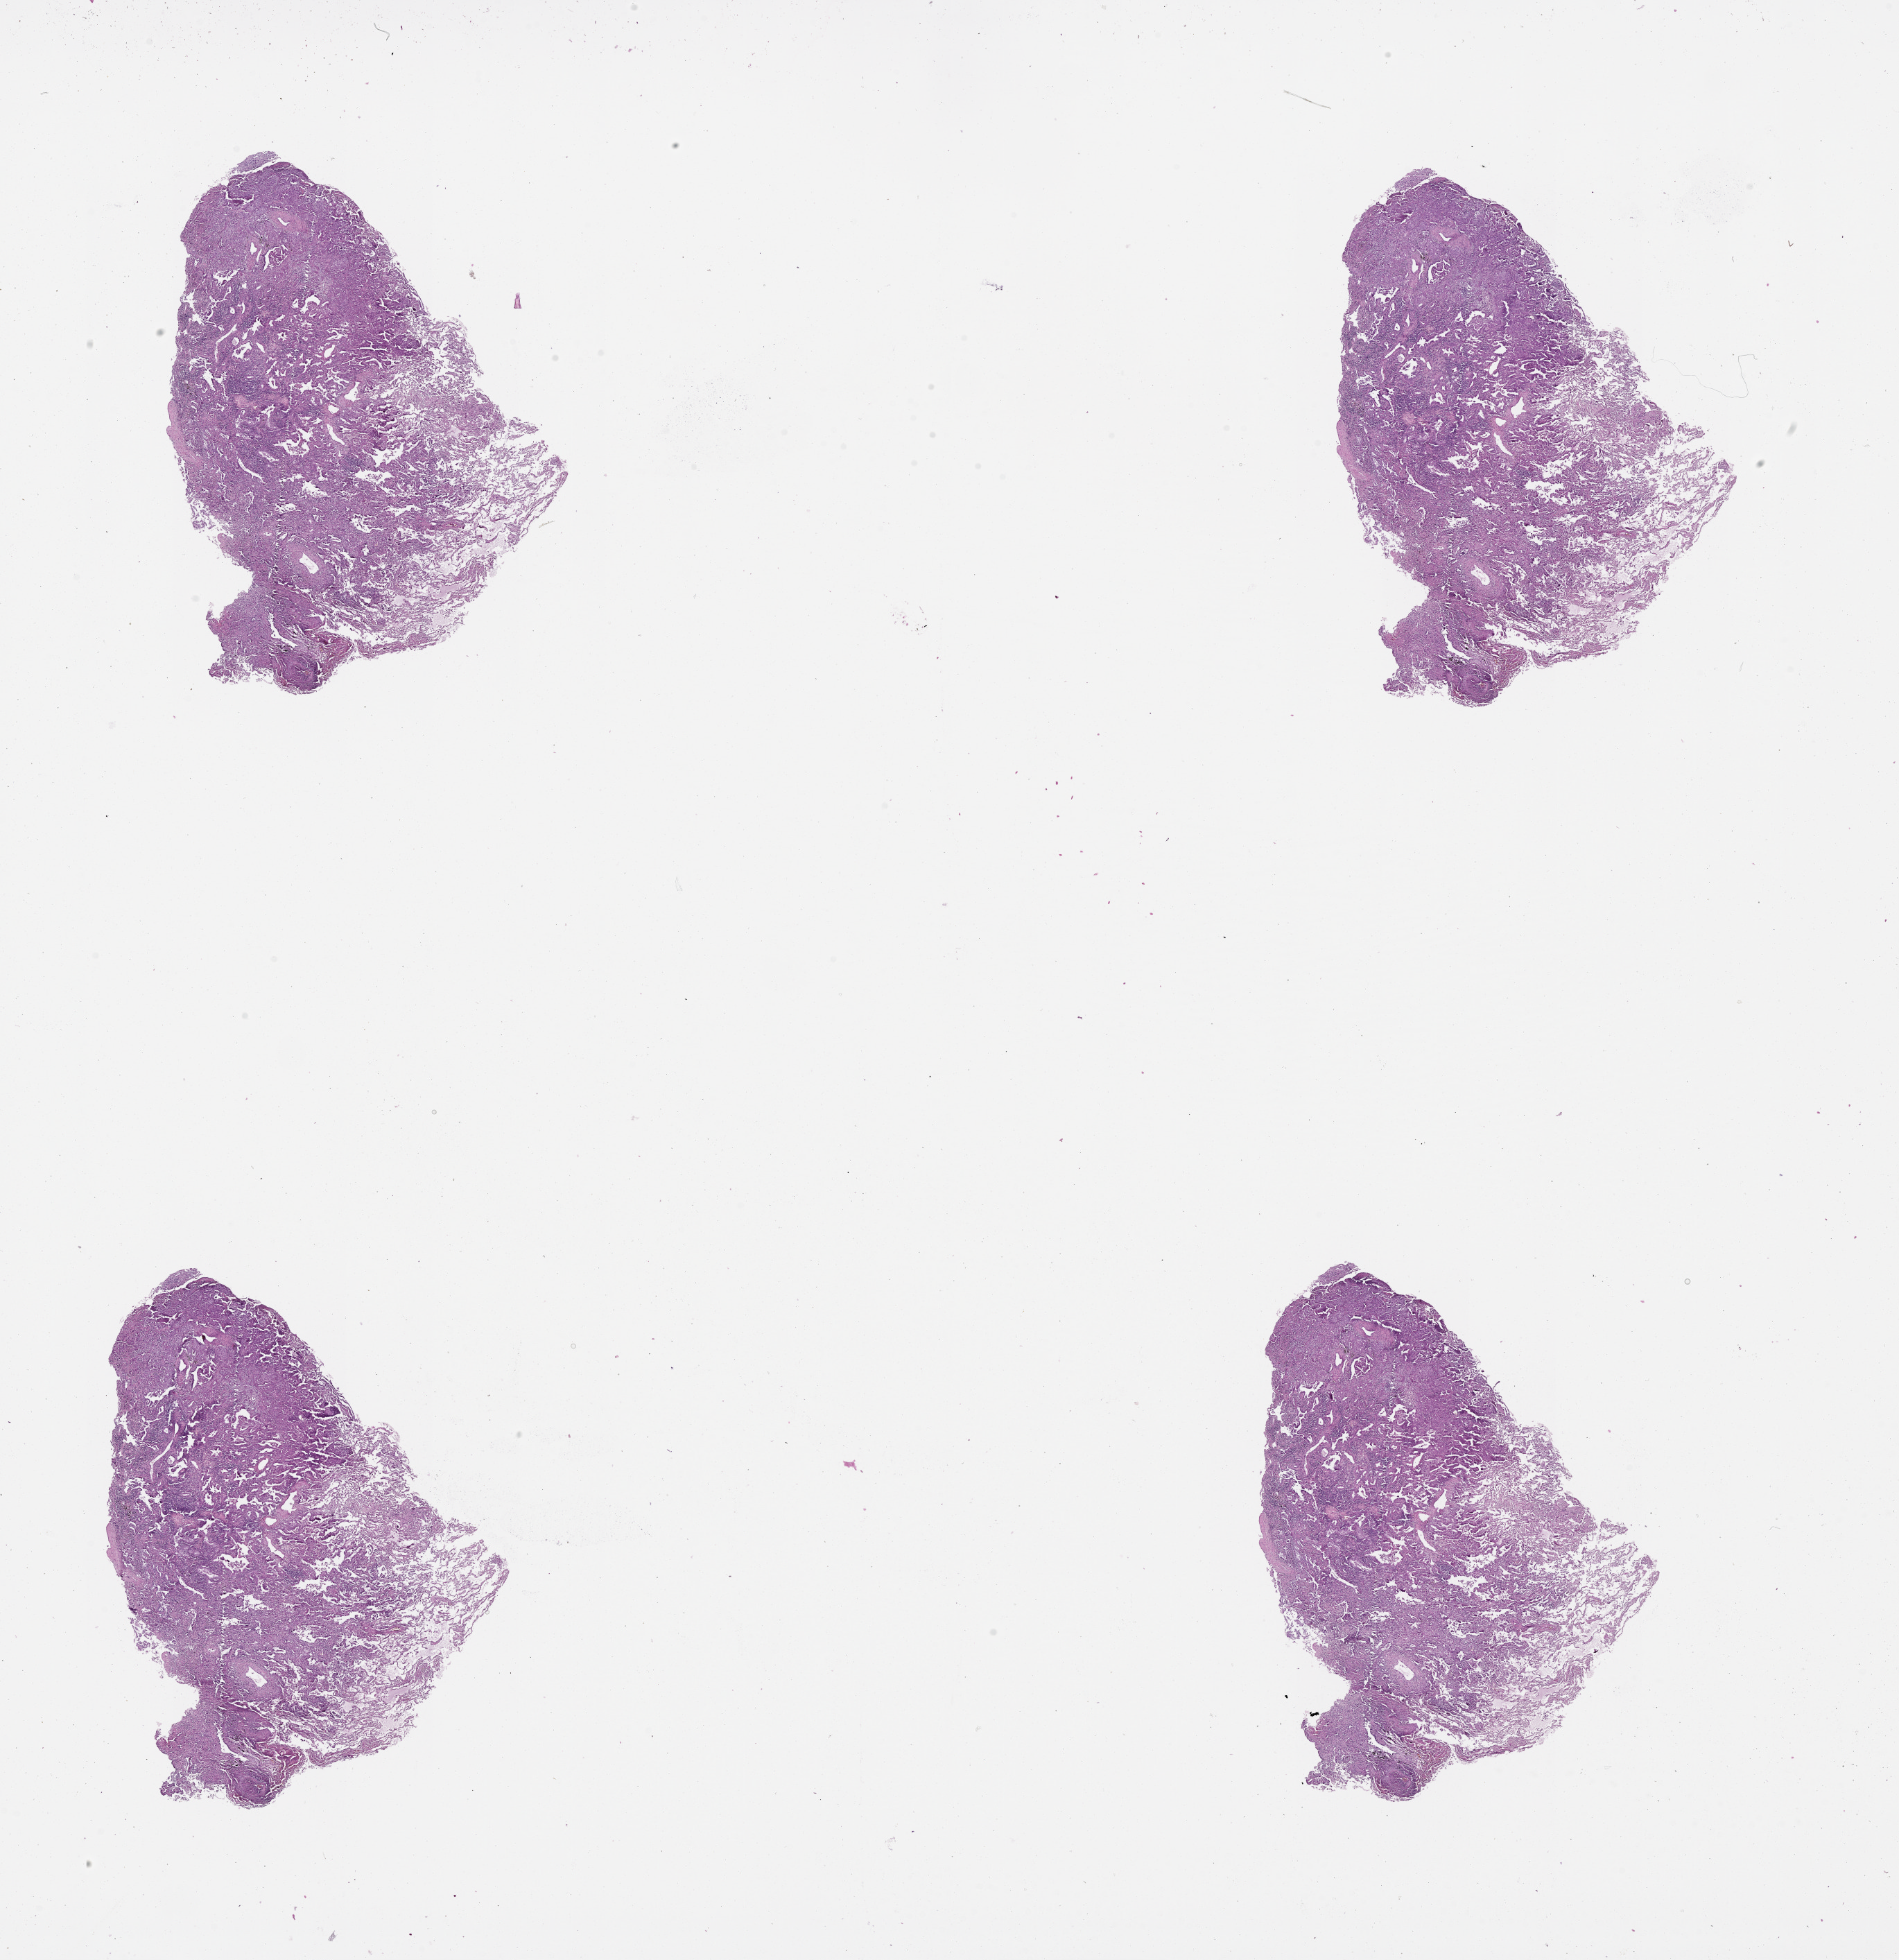
Digitized H&E tissue section (whole slide), a low-resolution overview of the entire scanned area, about 22.0 x 22.8 mm (slide scanned at 20x), lung, tumour tissue. 51-year-old female patient. Histologic grade: GX (grade cannot be assessed).
Primary tumour site (as recorded): left lower lobe. AJCC pathologic stage: IA. Histologic diagnosis: Adenocarcinoma, NOS.